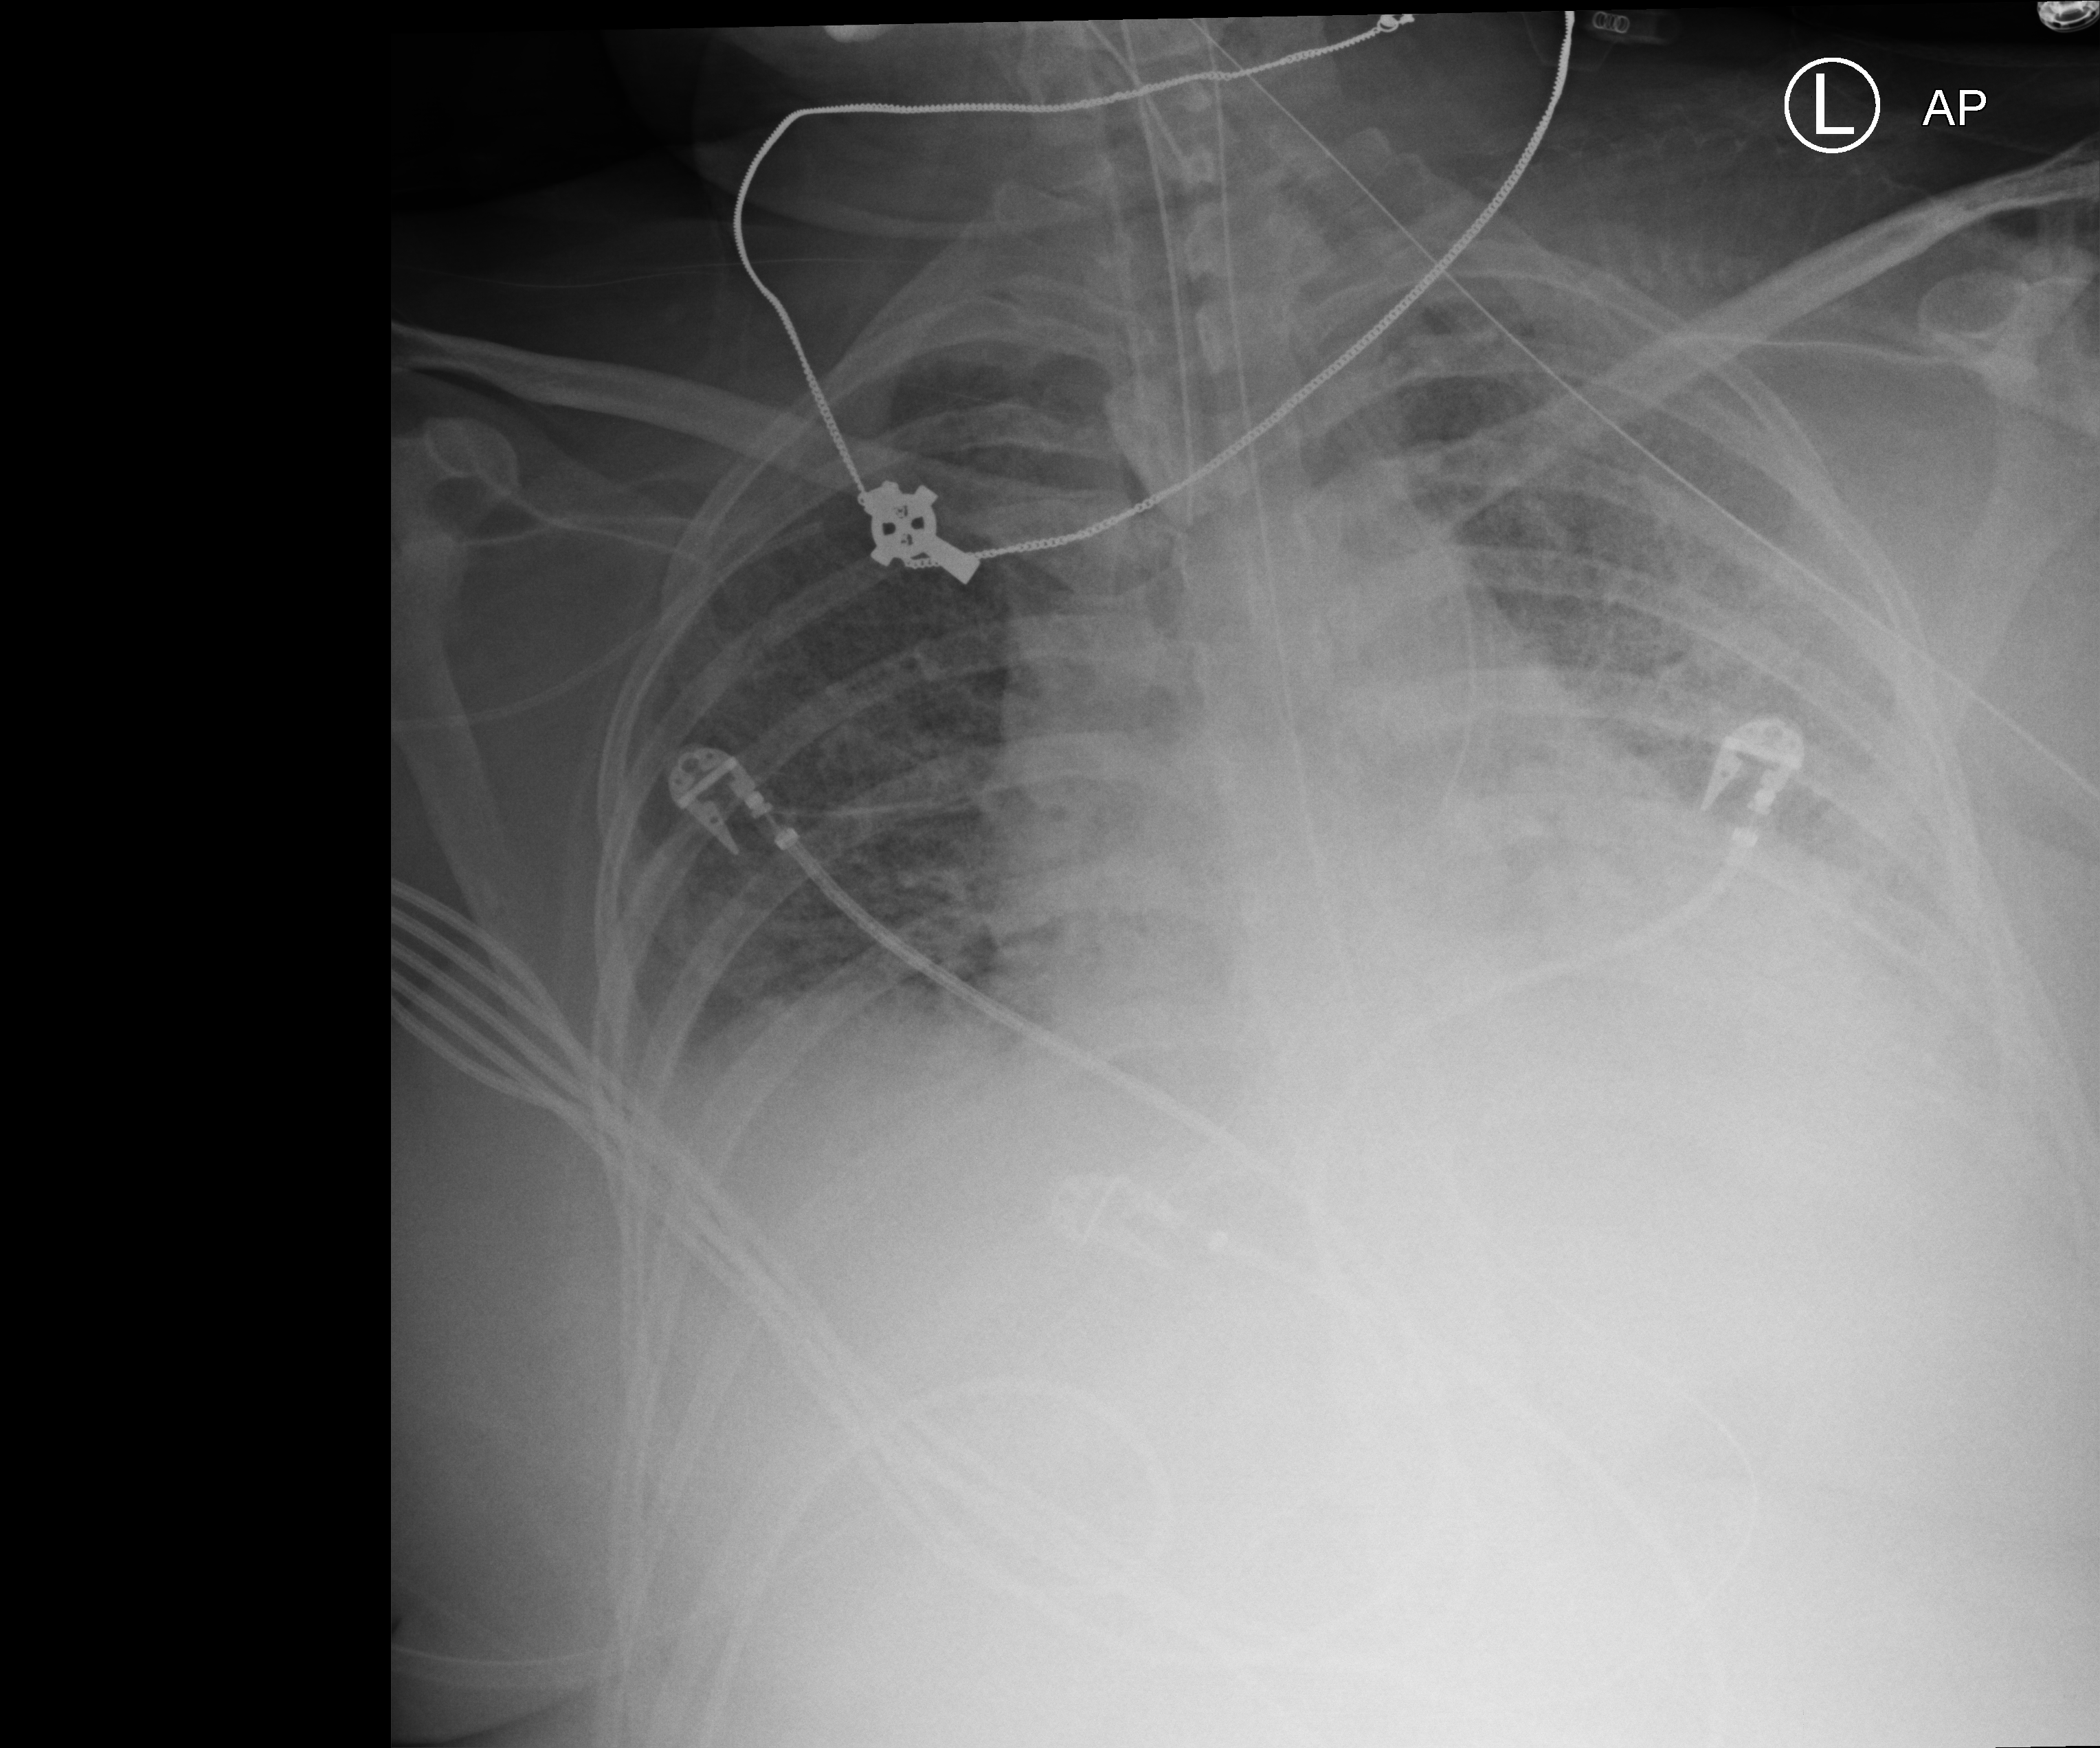
Bedside chest radiograph (computed radiography); anteroposterior (AP) projection. Female patient hospitalised with COVID-19, age 18–59 years.
Hospital-stay facts (about this admission, not read from this image; timing relative to this image not recorded):
- other chronic lung disease (admission record): yes
- diabetes (admission record): no